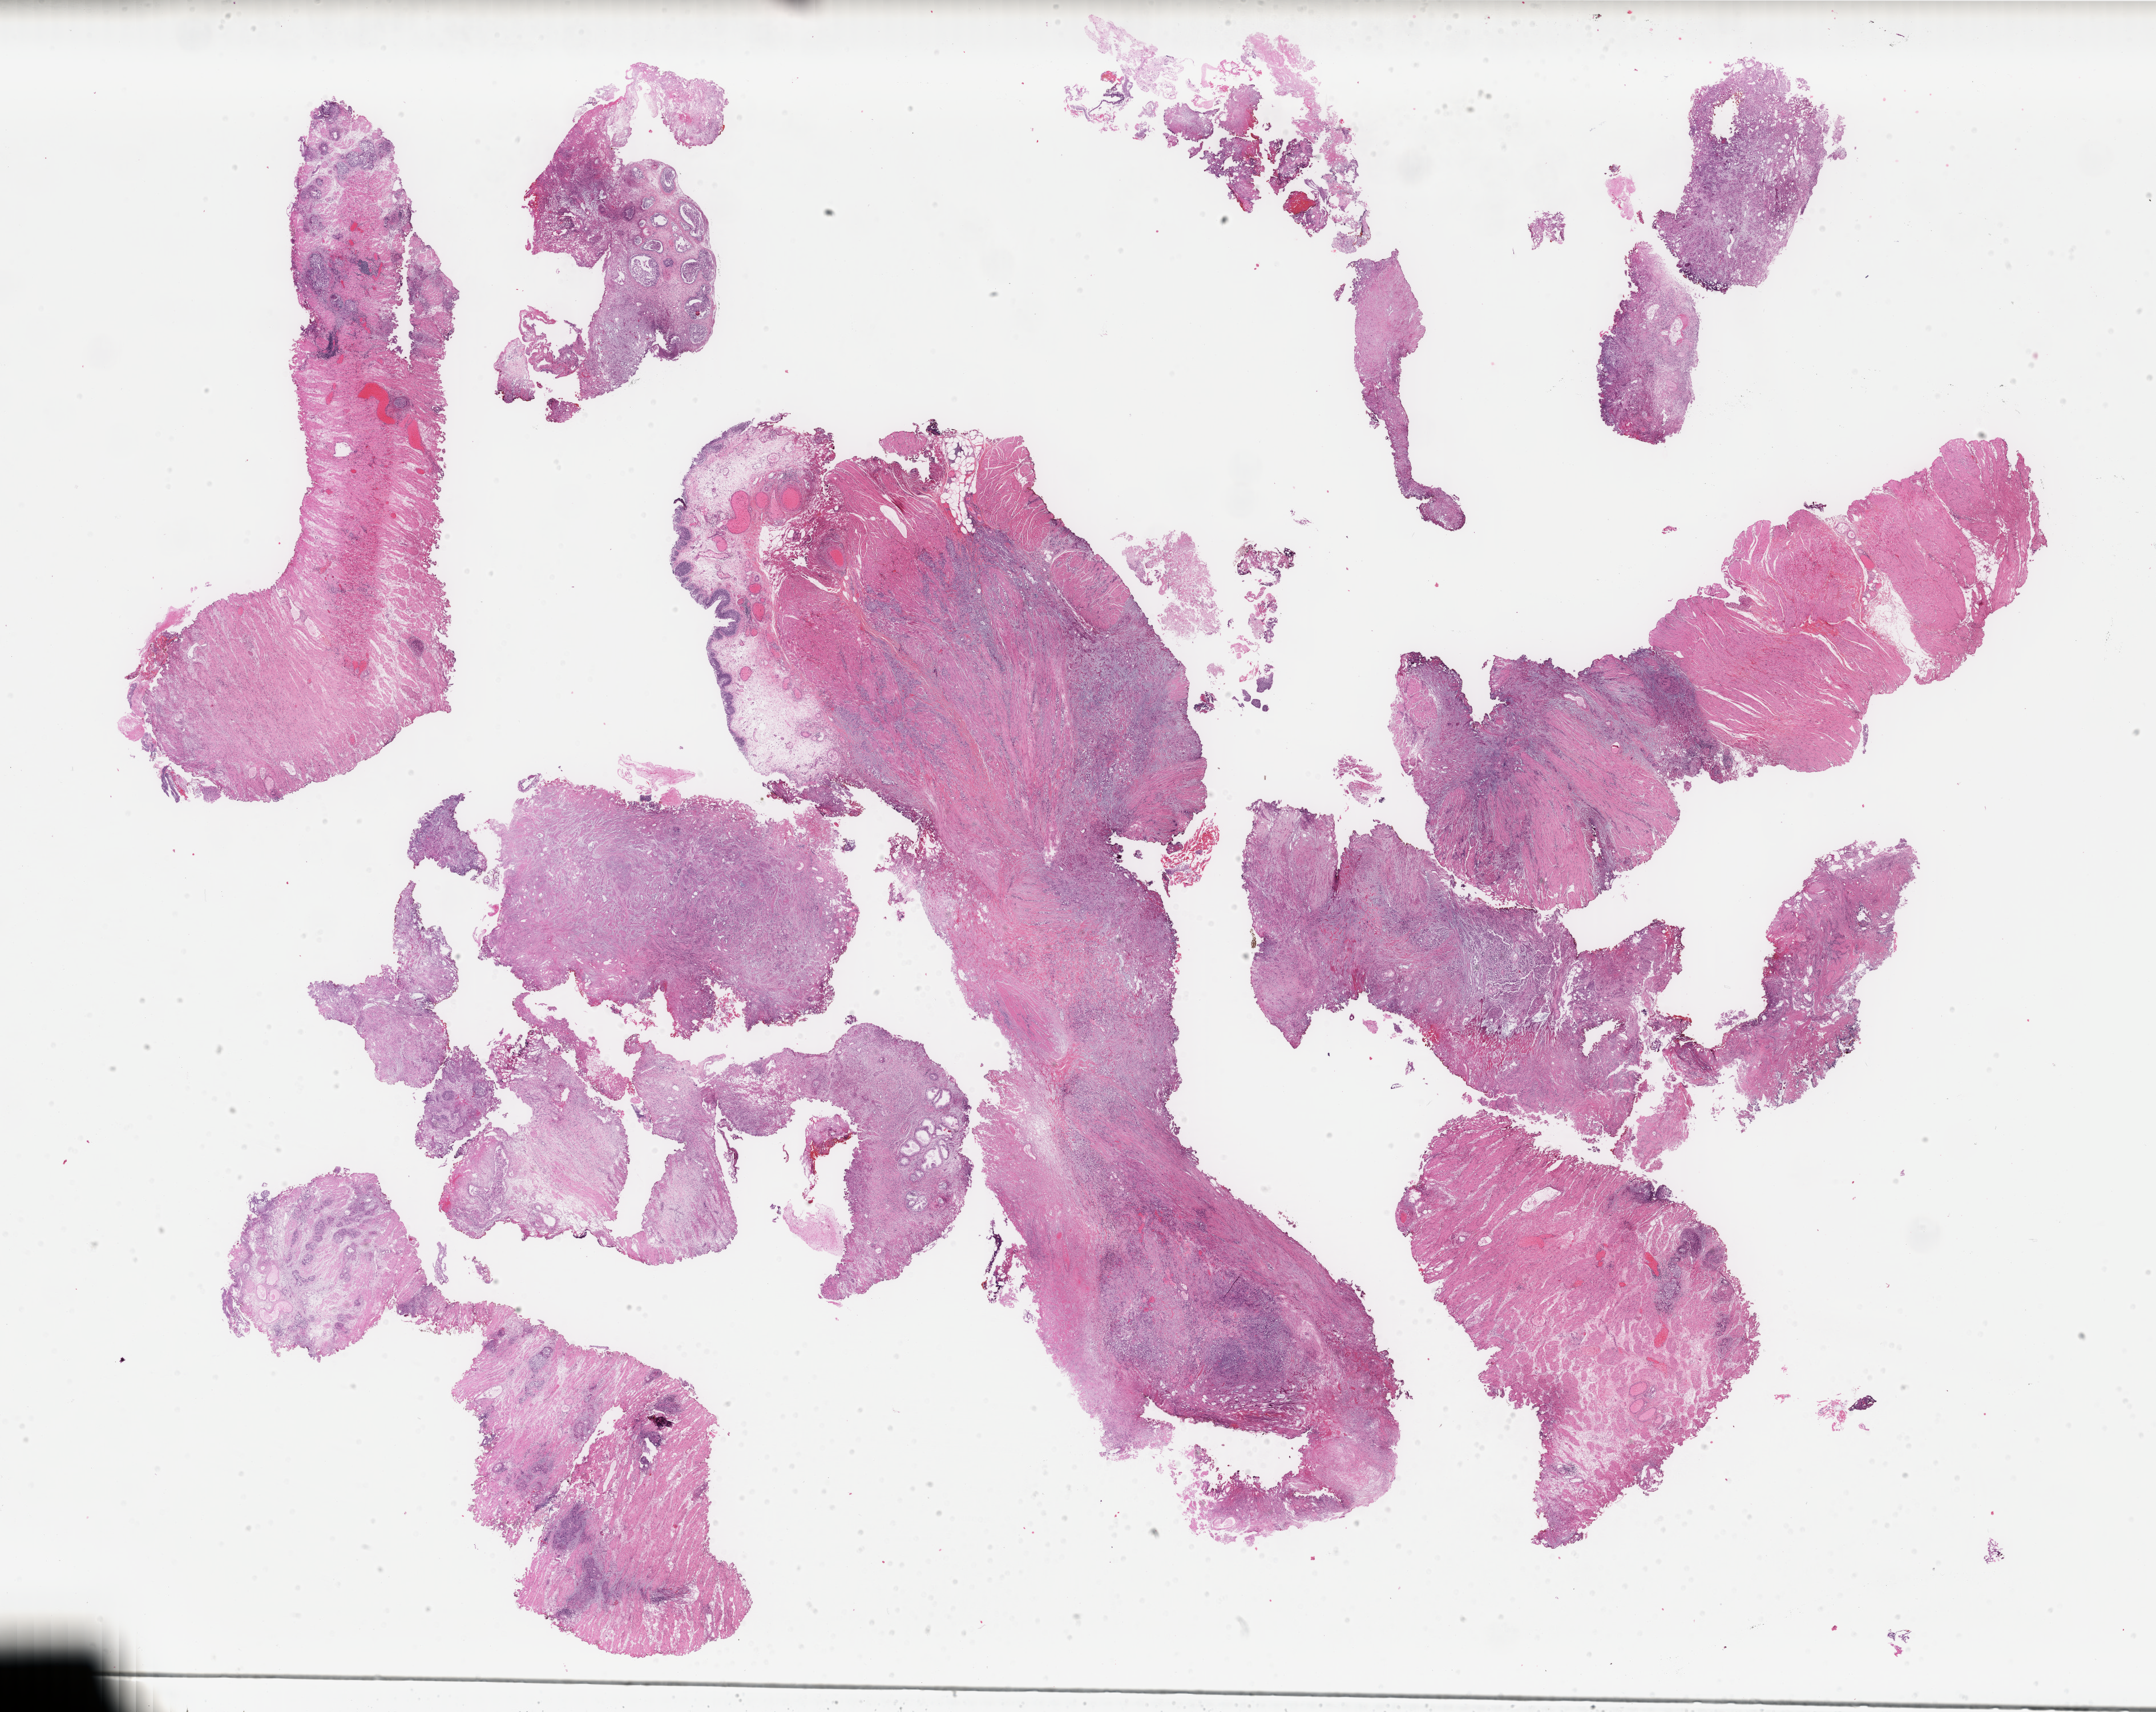
Digitized Hematoxylin and eosin (H&E) stained tissue section (whole slide), low-resolution overview of the scanned area, about 30.0 x 23.8 mm (slide scanned at 40x). Formalin-fixed paraffin-embedded (FFPE) diagnostic section. Primary tumour sample from the bladder. Male patient; age at initial diagnosis 57 years. Histologic grade: high grade.
AJCC pathologic stage: II. Diagnosis: Transitional cell carcinoma.